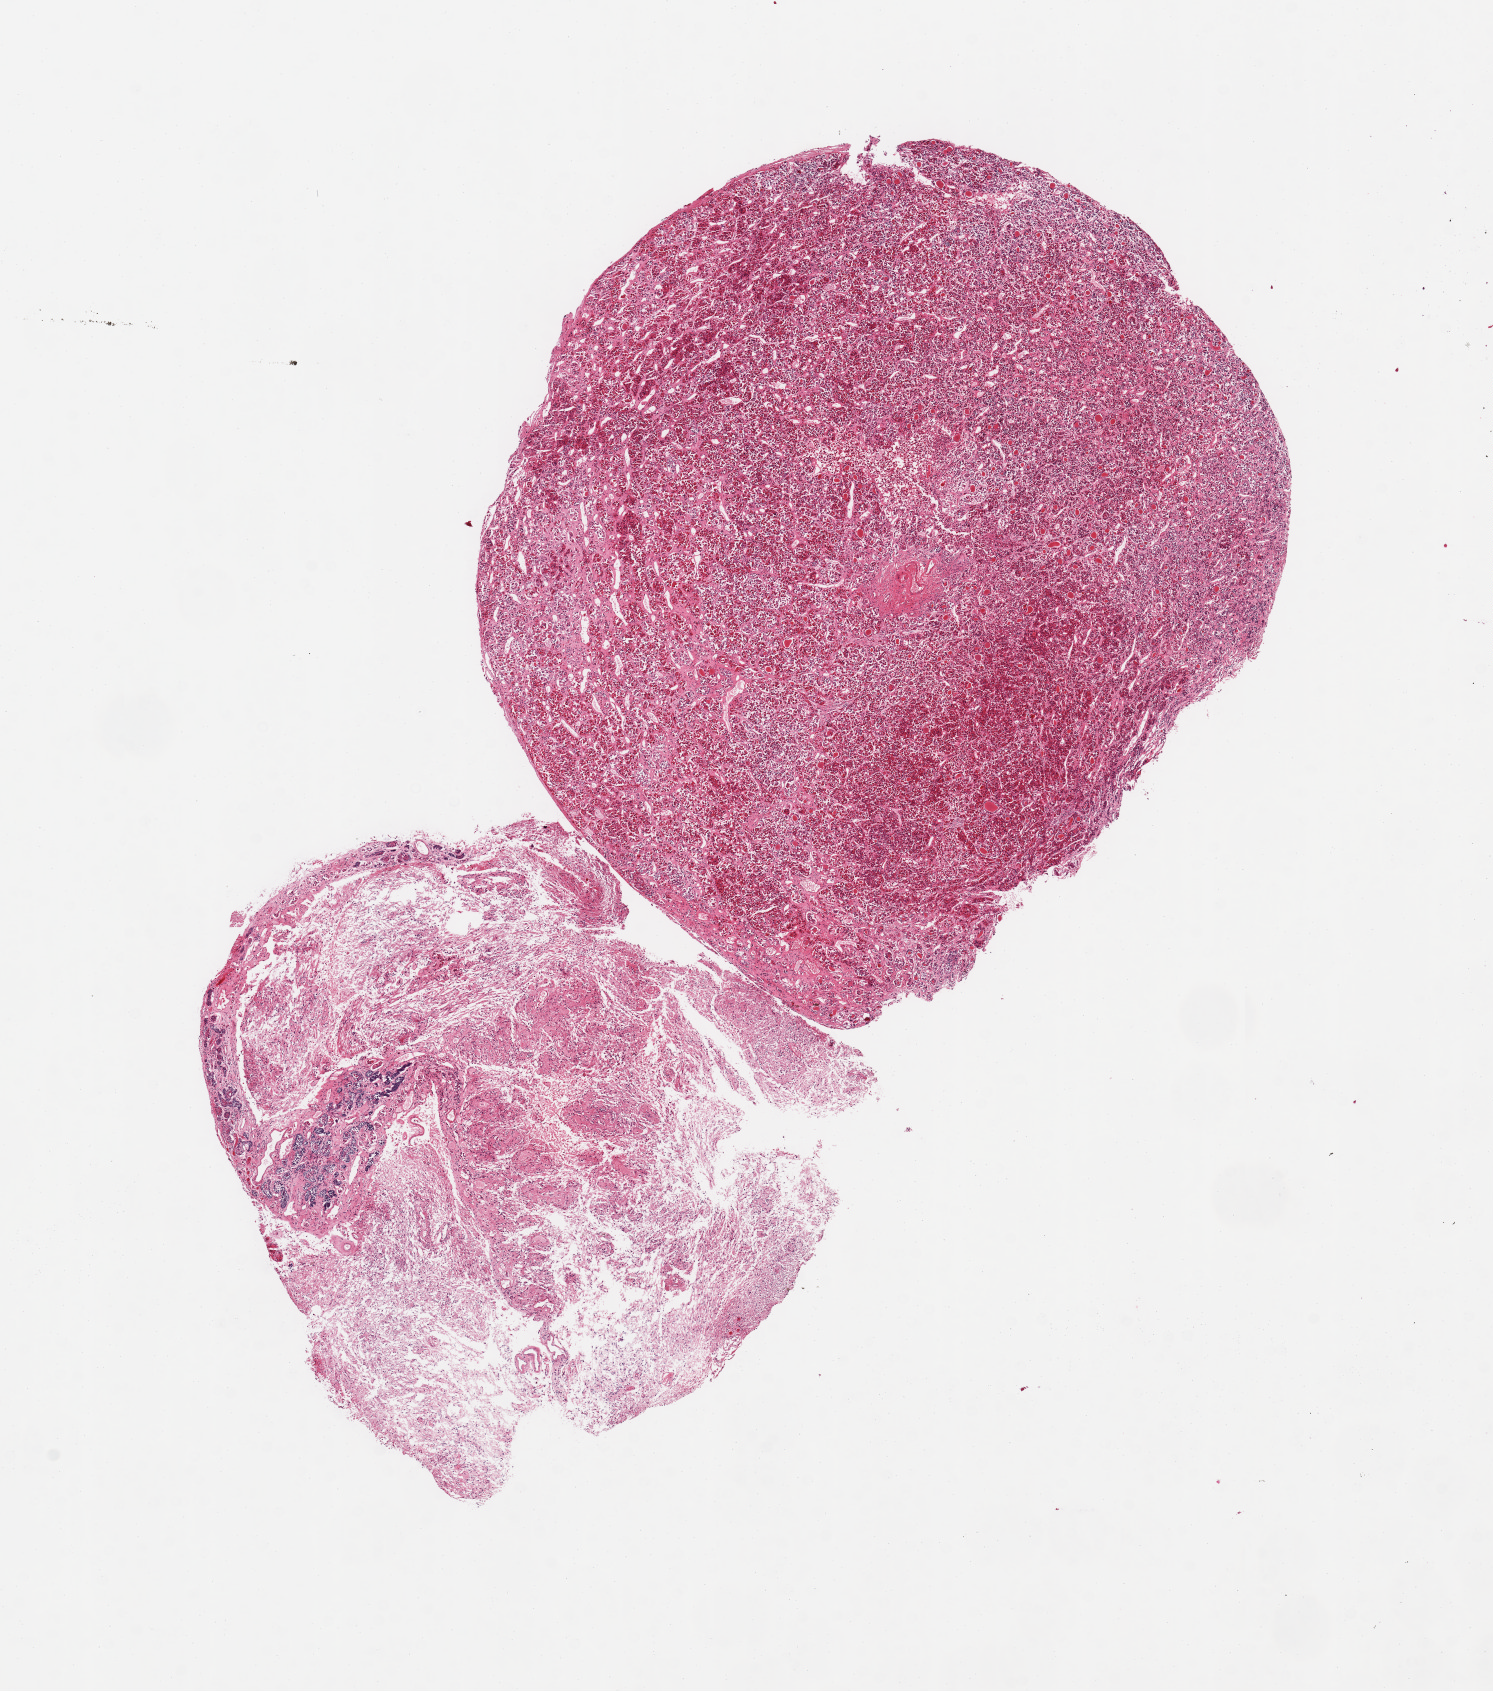
Whole-slide image, haematoxylin and eosin stain, low-resolution overview of the scanned area, about 11.8 x 13.4 mm; PAXgene-fixed, paraffin-embedded tissue; target tissue: pituitary; tissue donor sample.
- pathologist's review note for this sample: 2 pieces, one a ~5mm portion of neurohypophysis; rest is adenohypophysis